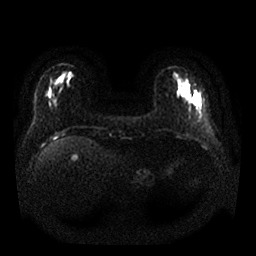
Breast MRI, one axial slice; slice 5 of 25 in the series (ordered by position); diffusion-weighted series; image 2 of 4 stored at this slice position (different b-values; order by instance number); 1.5 T; 4 mm slice thickness; 256 × 256 image matrix, field of view 340 × 340 mm. Female patient.
Structures marked on this image (expert manual segmentation):
- tumour on diffusion-weighted imaging: bounding box (x1, y1, x2, y2) in pixels: (185, 82, 203, 116)